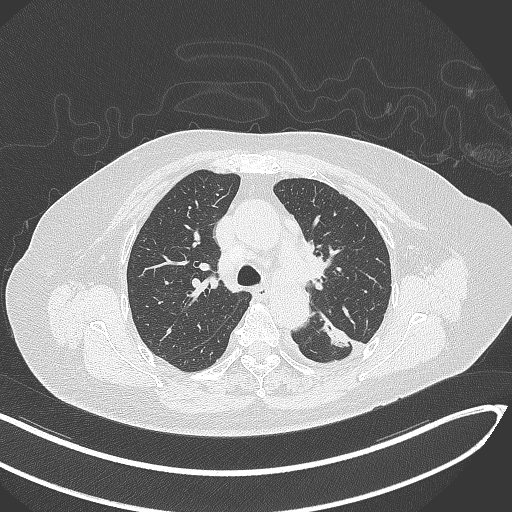
Chest CT, one axial slice; position 216 of 270 along the scan axis; reconstruction kernel B70f; 120 kVp; lung window (W 1500 / L -600 HU); 1 mm slice thickness; 512 × 512 image matrix, field of view 400 × 400 mm. Female patient, age 76 years. Case-level facts recorded for this patient, not image findings: clinical TNM (as recorded): T1c N0 M0.
Structures marked on this image (bounding box drawn by a radiologist):
- lung tumour (recorded histology: adenocarcinoma): bounding box <317,313,355,353> (left, top, right, bottom; pixels)